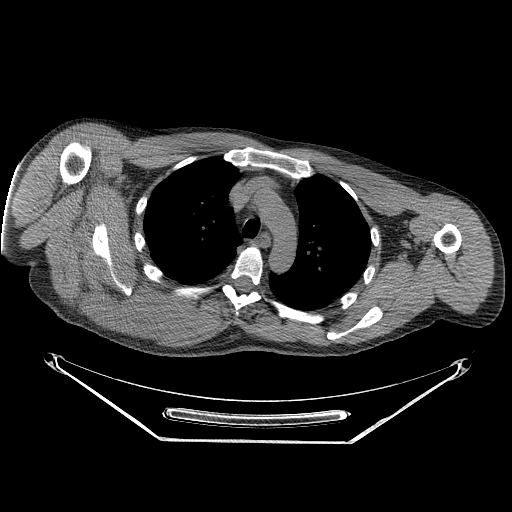
CT of an extremity soft-tissue mass (from a PET/CT study), one axial slice; slice 187 of 267 in the series (ordered by position); reconstruction kernel STANDARD; 140 kVp; soft-tissue window (W 400 / L 40 HU); 3.75 mm slice thickness; 512 × 512 image matrix, field of view 500 × 500 mm. Male patient. From the clinical record (not read from this slice): histological type: pleiomorphic spindle cell undifferentiated; grade: high; site of the primary tumour: right parascapusular.
Outlined on this slice (expert contour drawn on MRI and transferred to this co-registered scan by the dataset authors):
- gross tumour volume including surrounding oedema: box from (x=82, y=272) to (x=222, y=337) px
- gross tumour volume (mass): (x=84, y=274)–(x=202, y=334)